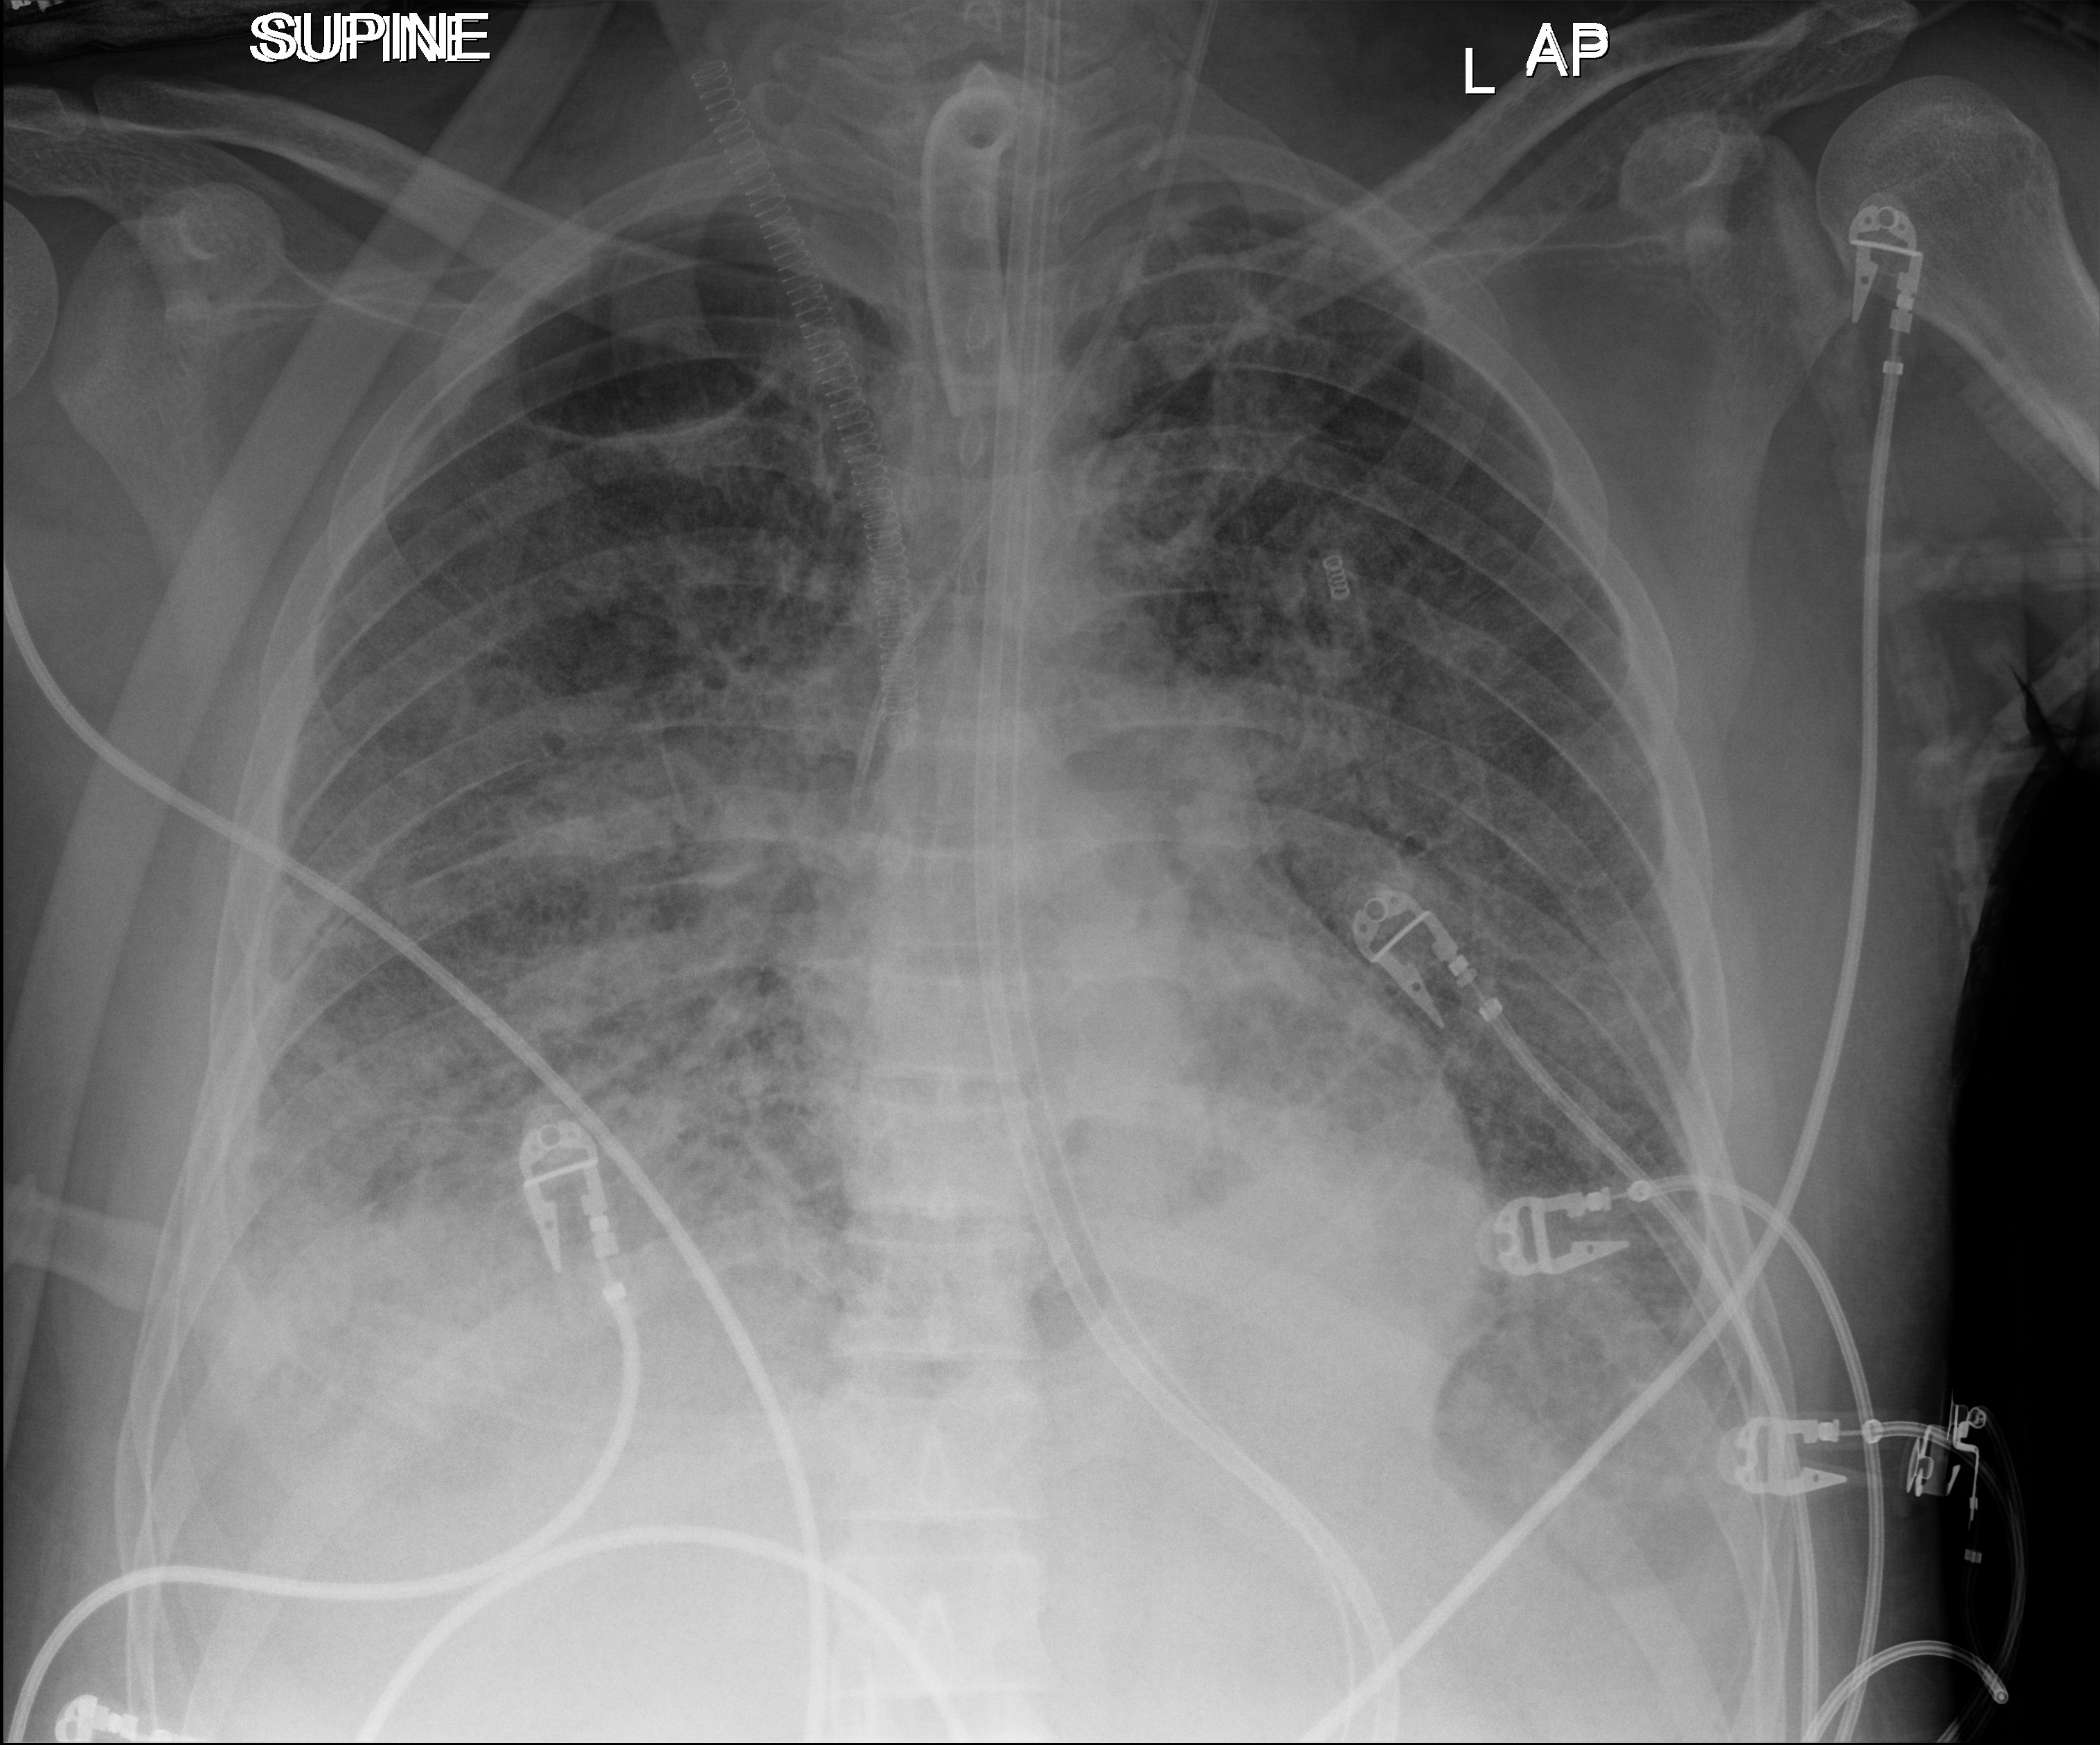
Portable chest radiograph; anteroposterior (AP) projection. Patient hospitalised with COVID-19, aged 18–59 years.
Hospital-stay facts (about this admission, not read from this image; timing relative to this image not recorded):
- mechanically ventilated during this hospital stay: yes